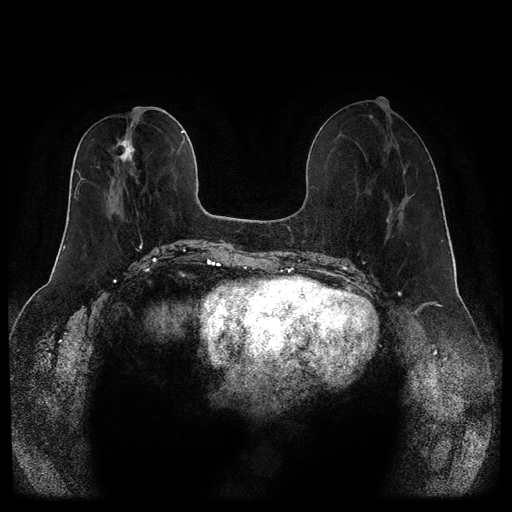
Breast MRI (dynamic contrast-enhanced, multi-phase), one axial slice. Position 42 of 116 along the scan axis. Dynamic contrast-enhanced series, time point 2 of 5 at this slice position (early post-contrast). 1.5 T. TE 2.6 ms, TR 5.3 ms. 2 mm slice thickness. 512 × 512 image matrix, field of view 350 × 350 mm. Patient: female, 46 years.
Outlined on this slice (semi-automatic segmentation, software-assisted and operator-edited):
- breast lesion (labelled 'tumour' in the annotation; benign lesions carry a separate 'benign' label): bounding box (x1, y1, x2, y2) in pixels: (114, 127, 136, 164)